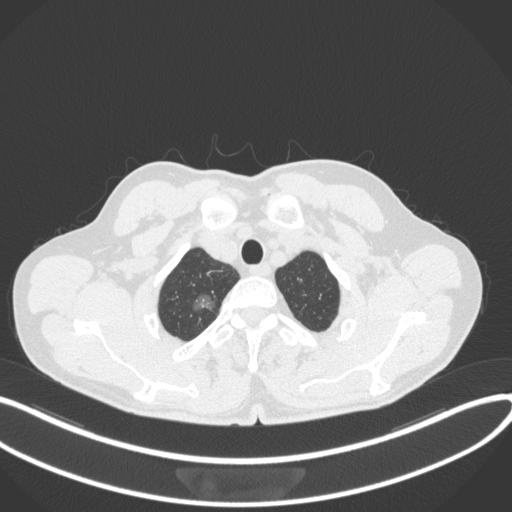
Chest CT, one axial slice; reconstruction kernel B31f; lung window (W 1500 / L -600 HU); 1 mm slice thickness; 512 × 512 image matrix. Male patient, age 58 years. From the clinical record (not read from this slice): clinical TNM (as recorded): T1c N0 M0; histopathological grade: G1-2.
Annotated regions visible in this slice (bounding box drawn by a radiologist):
- lung tumour (recorded histology: adenocarcinoma): bounding box <187,284,226,314> (left, top, right, bottom; pixels)